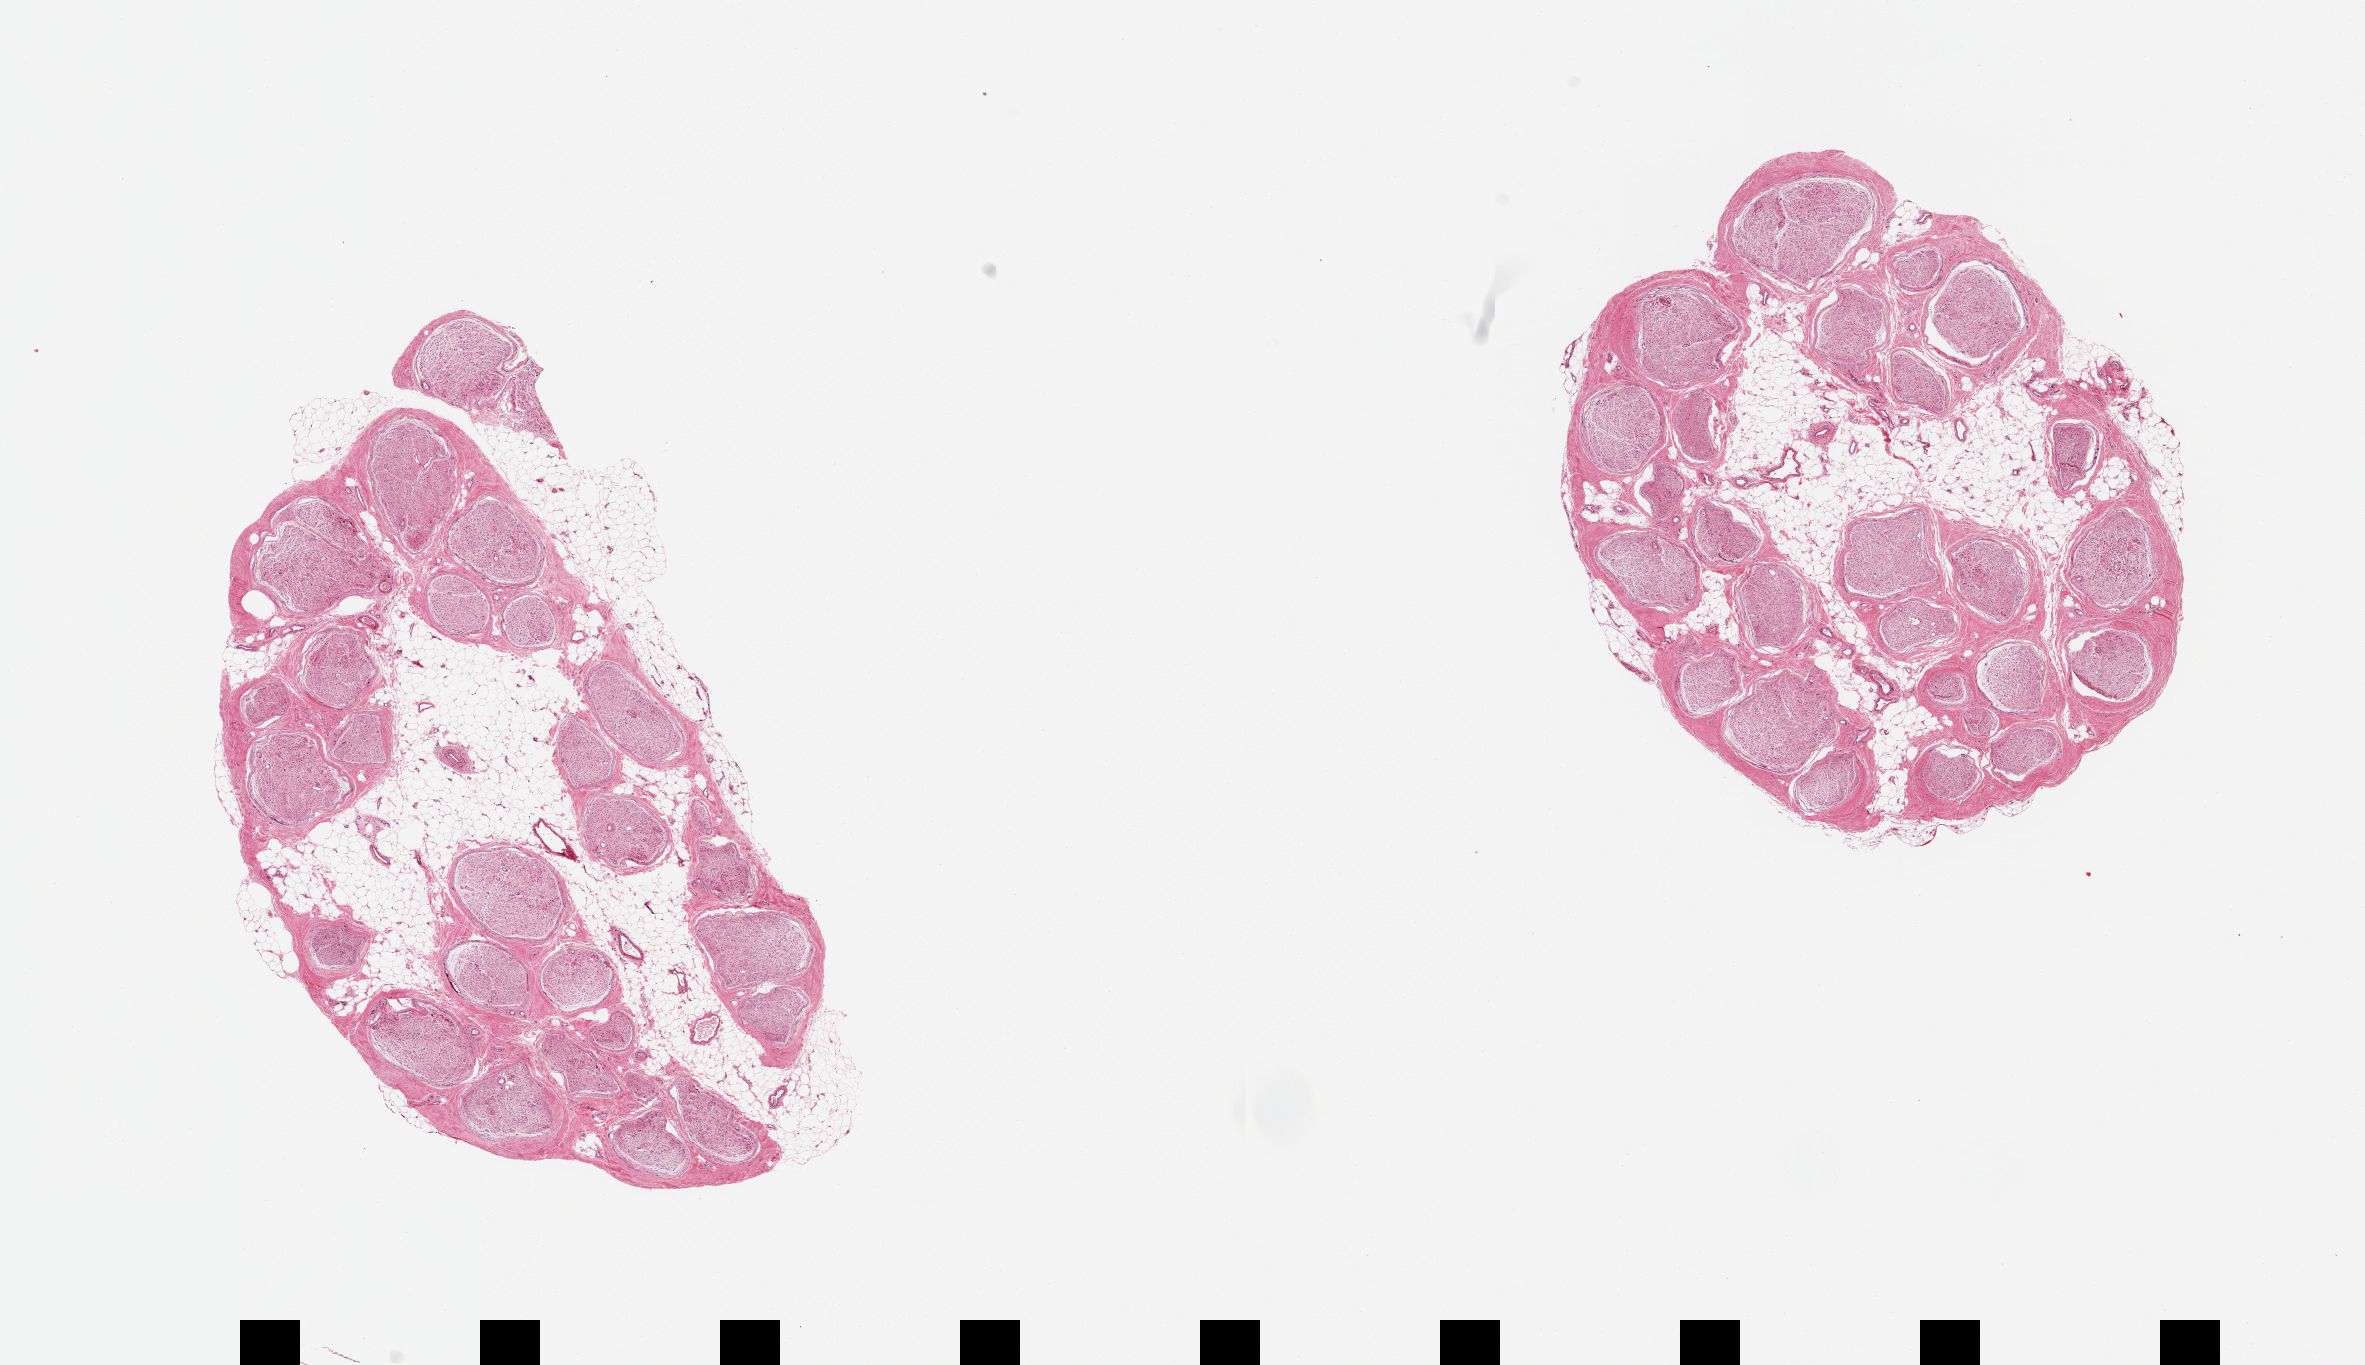
Digitized H&E-stained section — whole scanned area (about 18.7 x 10.8 mm, from a 20x scan) shown as a low-resolution overview. PAXgene-fixed, paraffin-embedded tissue. Section of tibial nerve (target tissue). Donor tissue sample. Donor: male.
Reviewer comment on this tissue sample: 2 pieces; 40% & 30% internal fat.